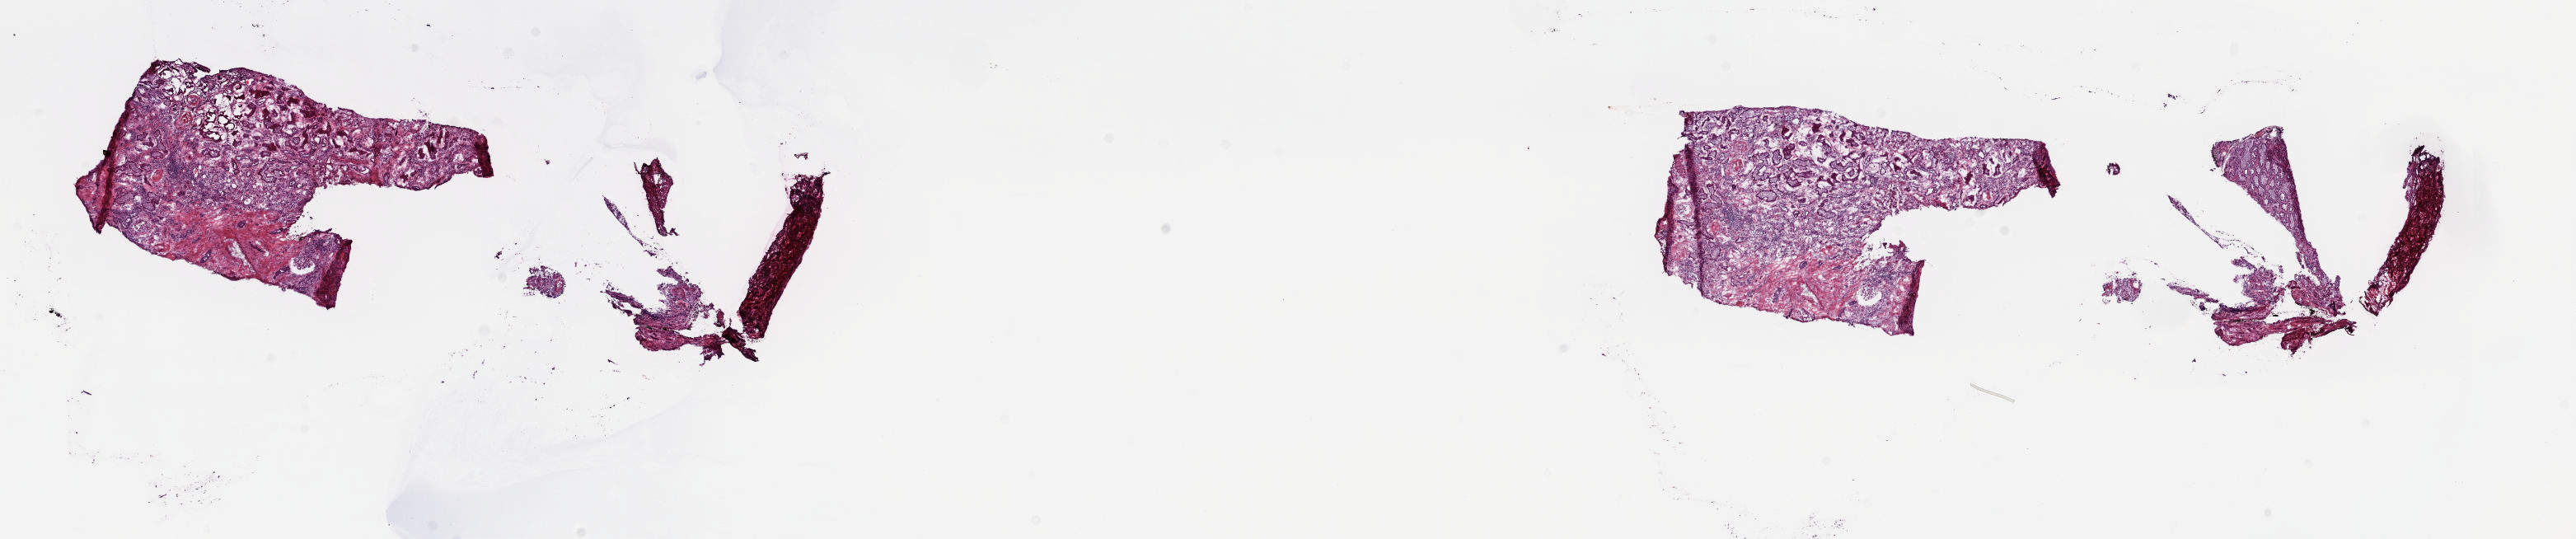
Digitized Hematoxylin and eosin (H&E) stained tissue section (whole slide), low-resolution overview of the scanned area, about 24.8 x 5.2 mm (acquisition: 20x scan); frozen section; kidney, solid tissue normal (non-tumour tissue) sample. Male patient; age at initial diagnosis 55 years.
This section: solid tissue normal sample (biorepository sample class). Patient diagnosis: Papillary adenocarcinoma, NOS.